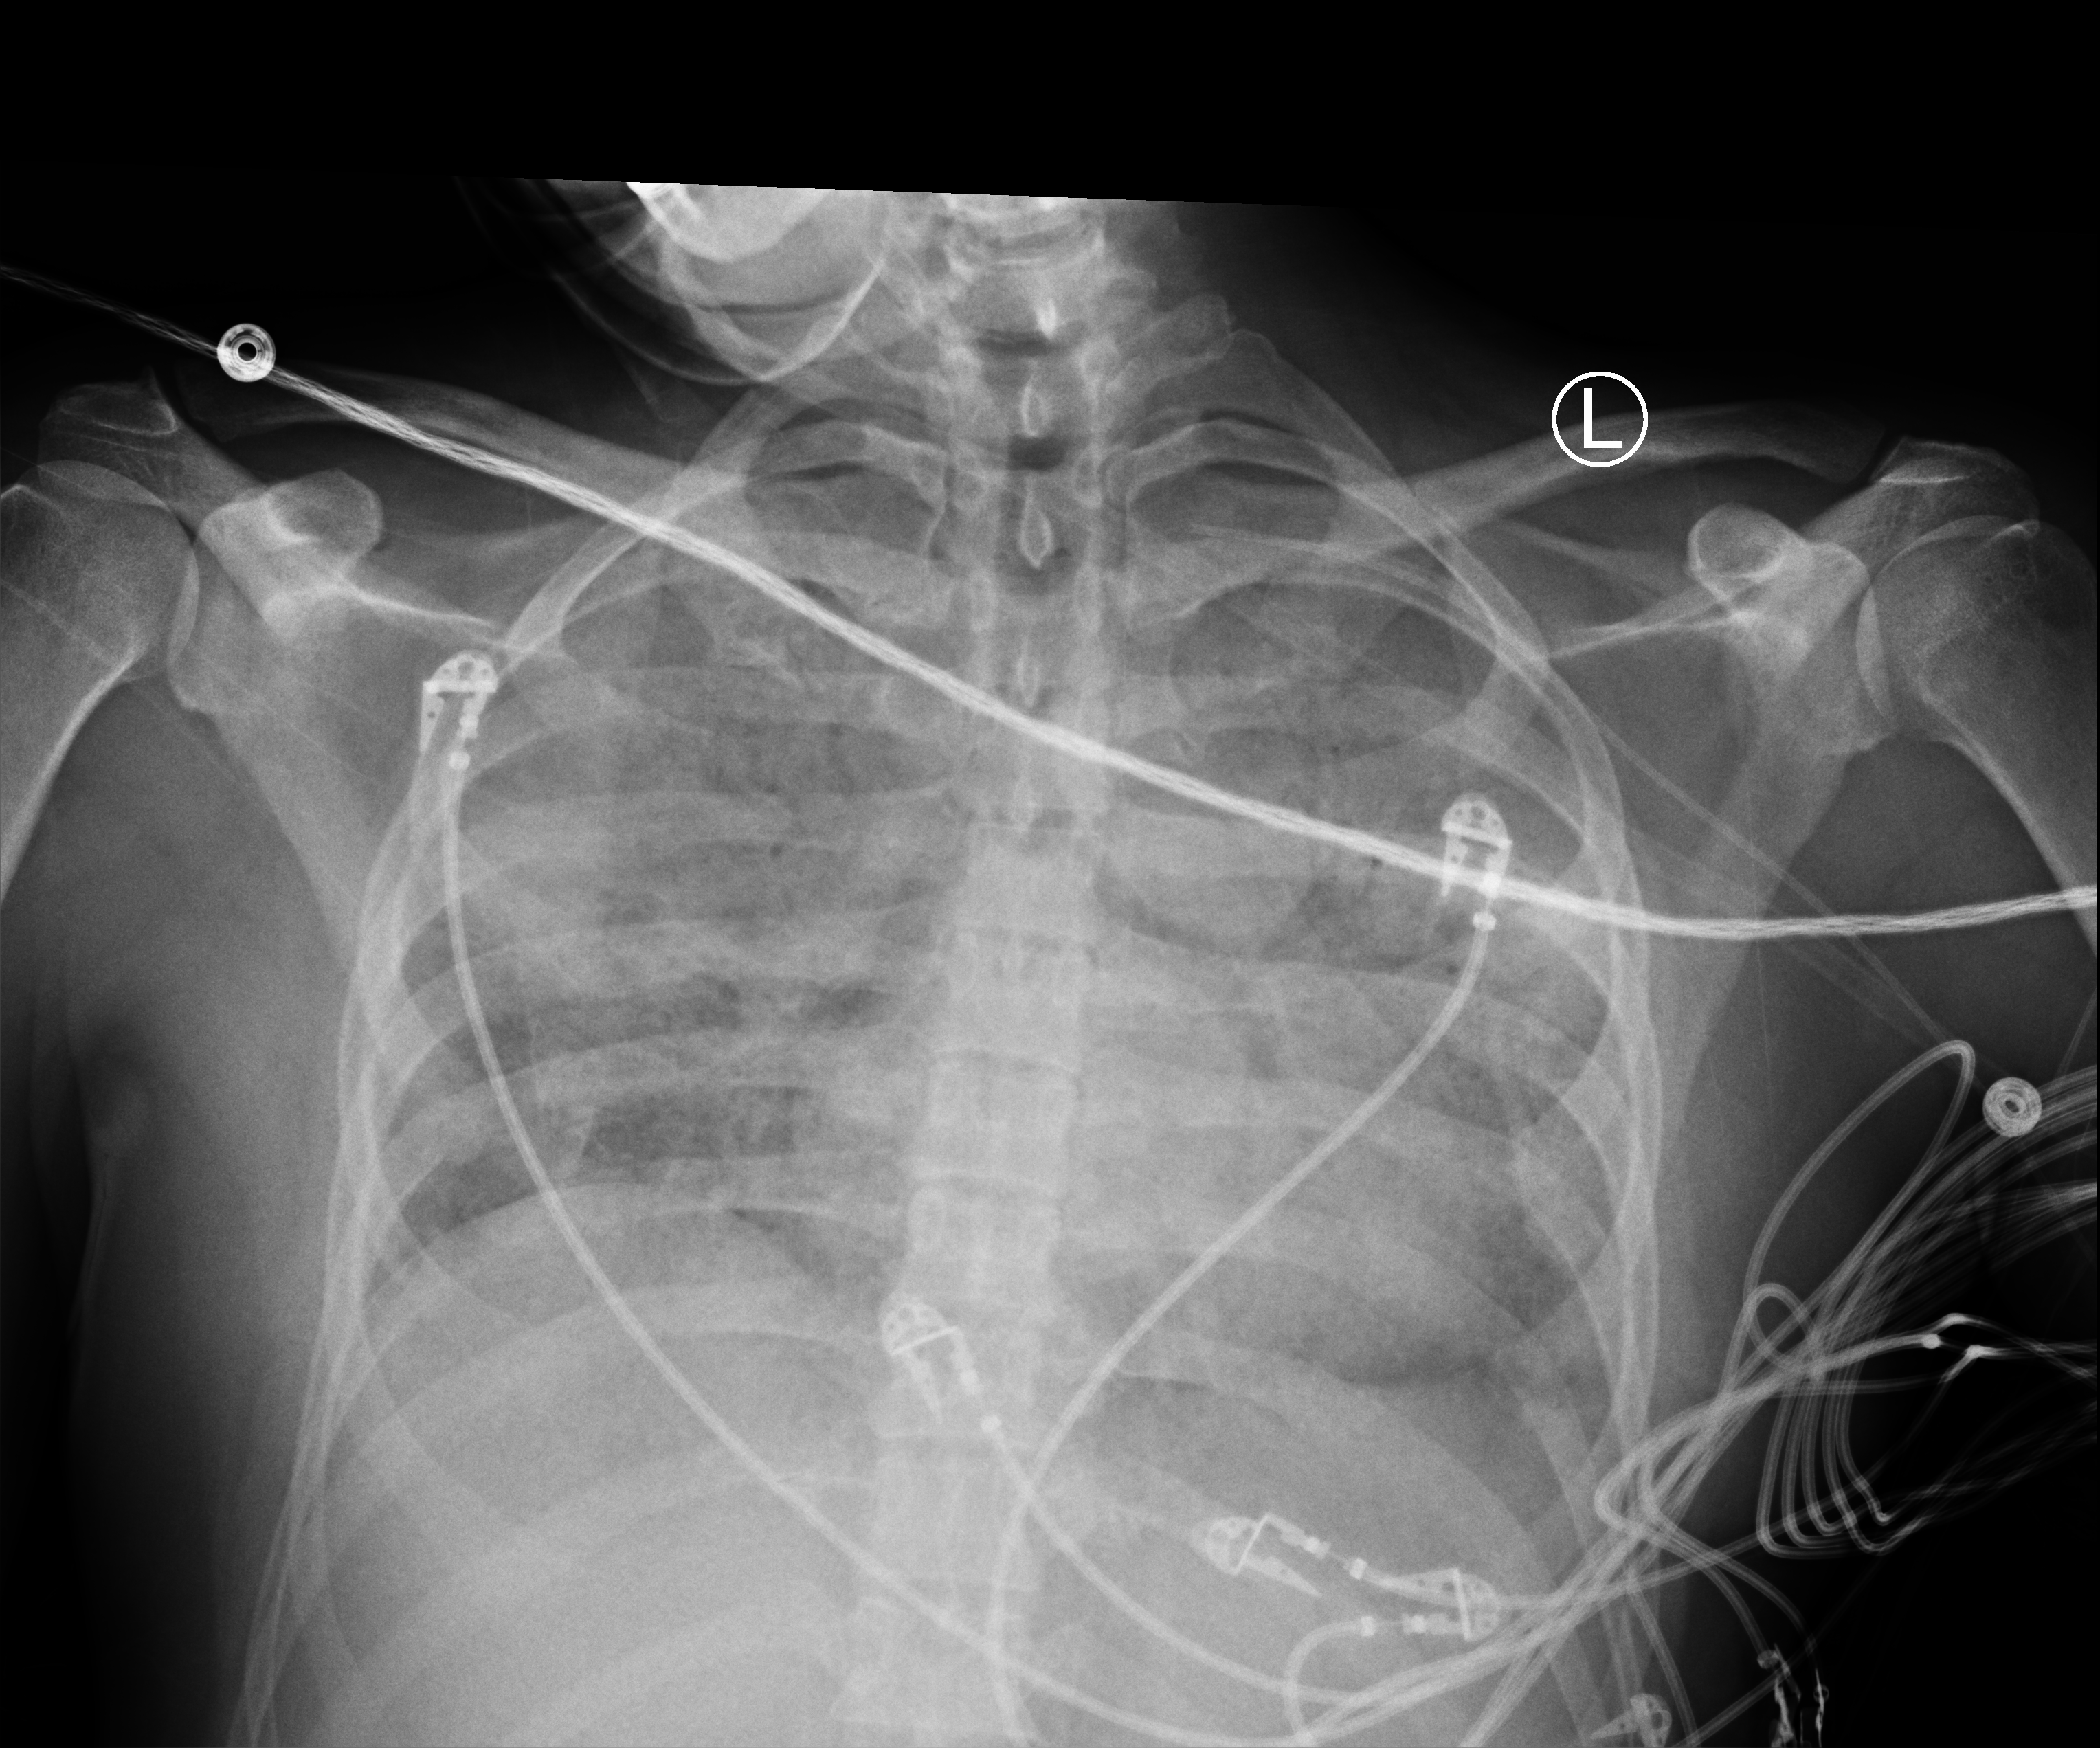
Bedside chest radiograph (computed radiography), anteroposterior (AP) projection. Male patient hospitalised with COVID-19, age 18–59 years.
From the hospital-stay record, not from the radiograph (when in the stay this image was taken is not recorded): admitted to intensive care during this hospital stay: yes; COPD (admission record): no; mechanically ventilated during this hospital stay: yes.